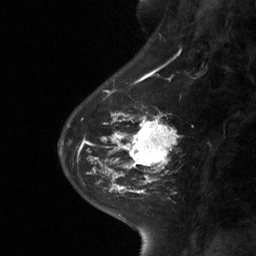
Breast MRI (dynamic contrast-enhanced), one sagittal slice; position 22 of 64 along the scan axis; dynamic contrast-enhanced study with each time point stored as its own series, time point 2 of 3 at this slice position (early post-contrast, ordered by acquisition time); 1.5 T; TE 4.8 ms, TR 27 ms; 256 × 256 image matrix. Patient: female, 42 years. Case-level facts recorded for this patient, not image findings: setting: breast cancer imaged before/during neoadjuvant chemotherapy; receptor status: triple-negative.
Outlined on this slice (semi-automatic segmentation, software-assisted and operator-edited):
- analysis volume of interest (the breast-tissue region the enhancement analysis was run in; not a lesion): bounding box [x1, y1, x2, y2] px = [111, 104, 177, 178]
- tumour enhancement mask (voxels above the 90 % enhancement threshold inside the analysis volume of interest): [111, 112, 176, 178]